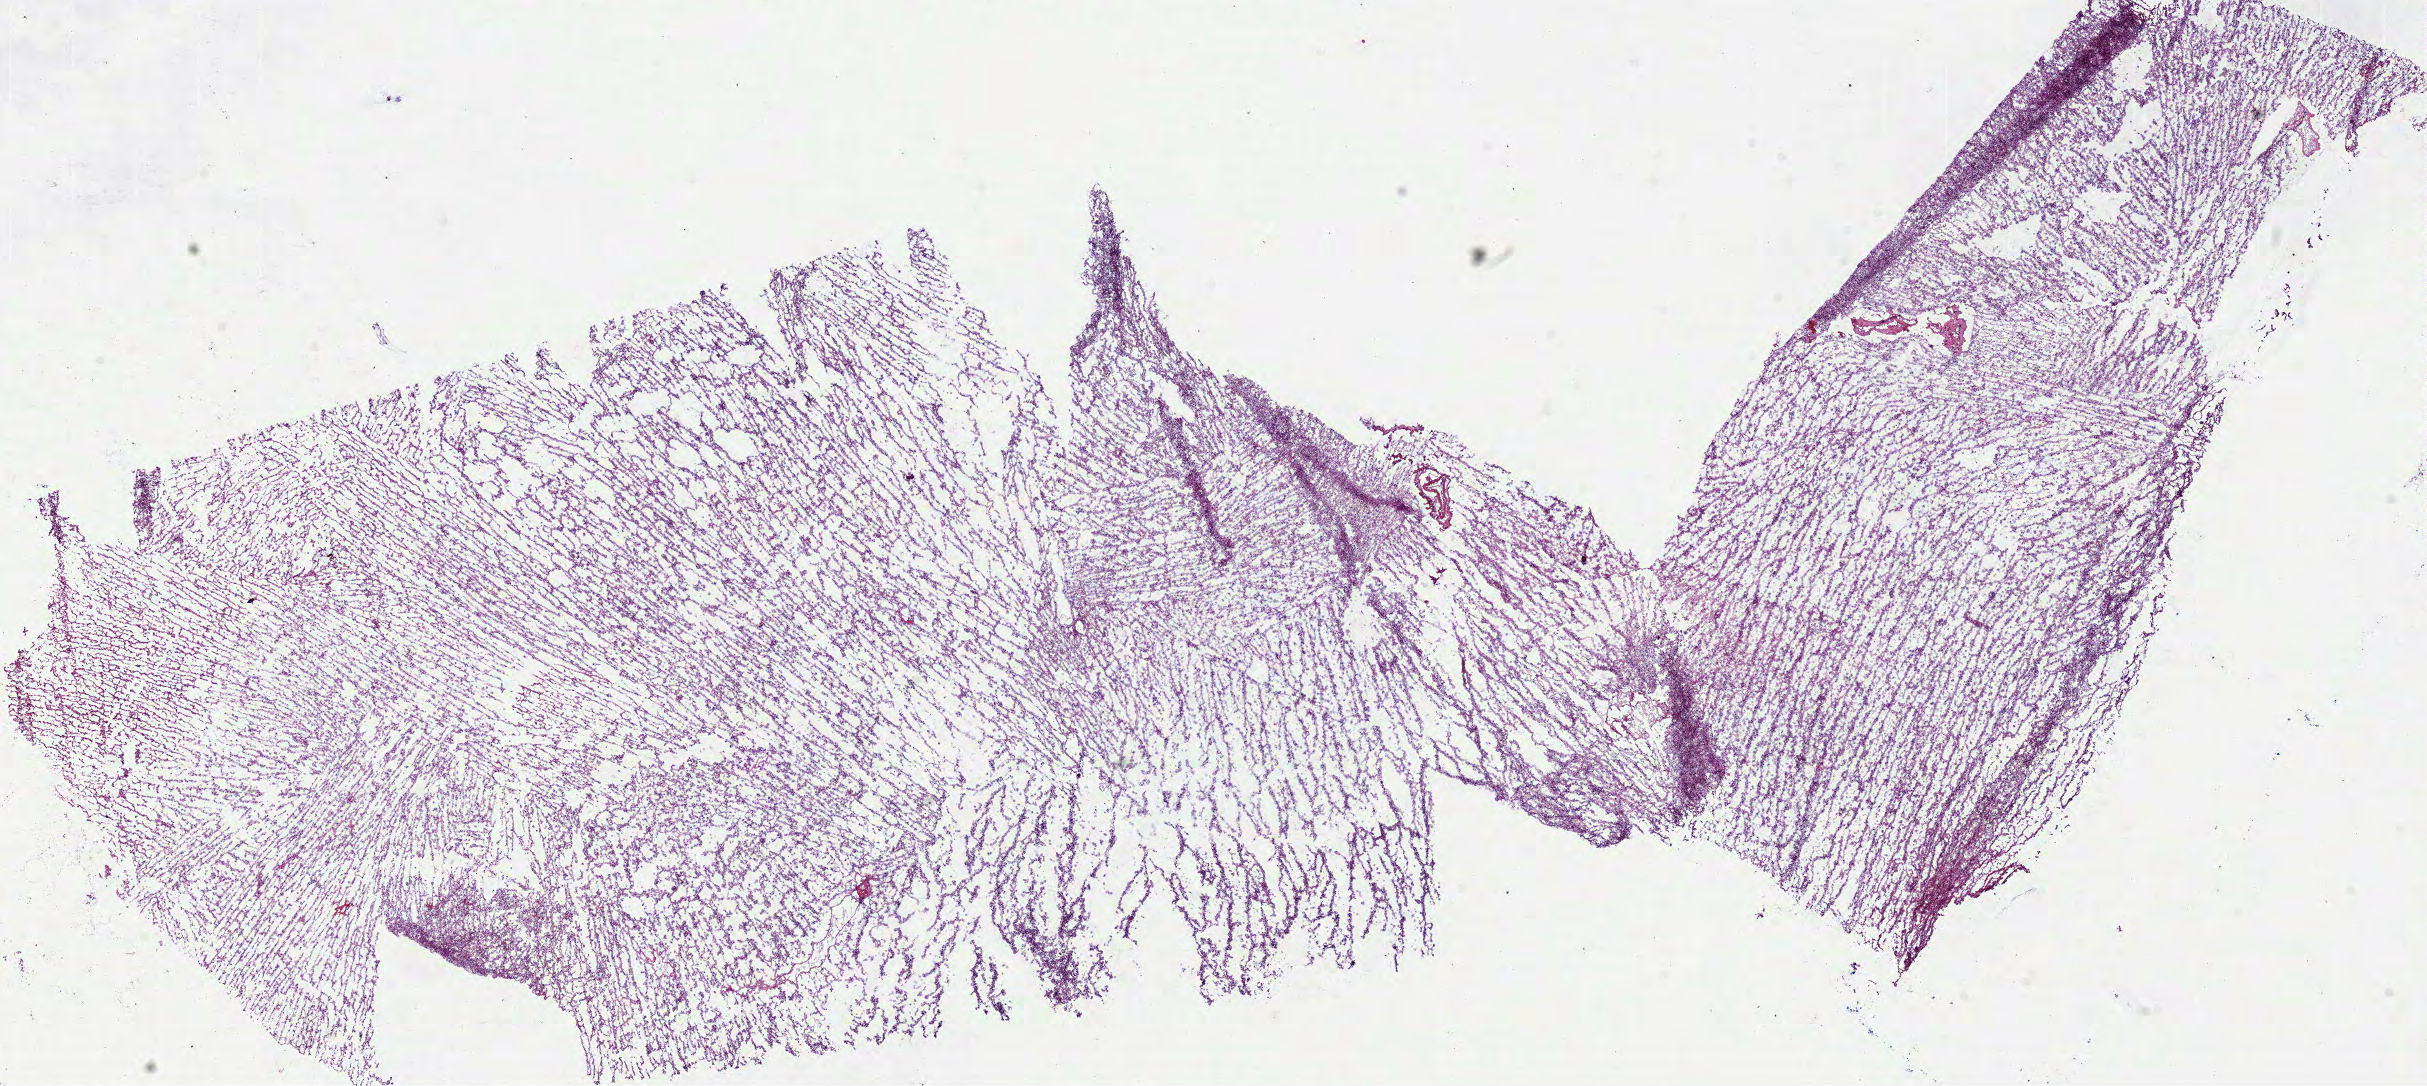
Digitized H&E-stained tissue section (whole slide), a low-resolution overview of the entire scanned area, about 19.6 x 8.8 mm, frozen section from the bottom of the tissue portion, sample: primary tumour, brain. Male patient; age at initial diagnosis 22 years. Histologic grade: G3 (poorly differentiated). Pathologist review of this section (percent, as recorded): tumour cells 100%, tumour nuclei 75%, normal cells 0%, stromal cells 0%, necrosis 0%.
* diagnosis: Astrocytoma, anaplastic